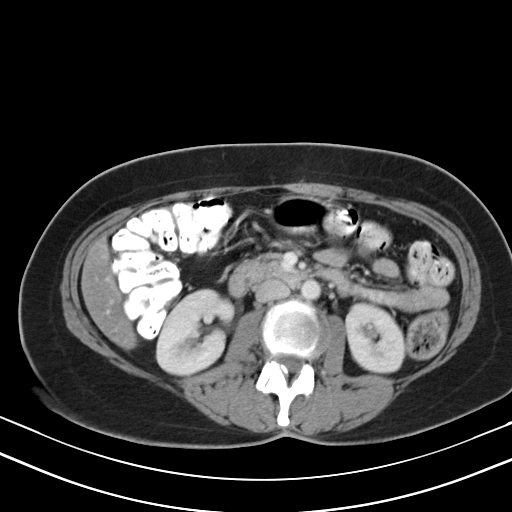
Contrast-enhanced abdominal CT, one axial slice. Position 17 of 47 along the scan axis. 130 kVp. Soft-tissue window (W 400 / L 40 HU). 5 mm slice thickness. 512 × 512 image matrix, field of view 350 × 350 mm. Female patient. From the clinical record (not read from this slice): diagnosis: colorectal cancer liver metastases, imaged before liver resection; multiple liver metastases: no; largest metastasis: 3.5 cm.
Annotated regions visible in this slice (manually delineated by an expert):
- liver: bounding box [x1, y1, x2, y2] px = [83, 243, 133, 346]
- planned liver remnant (the part of the liver to remain after resection): [83, 243, 133, 345]